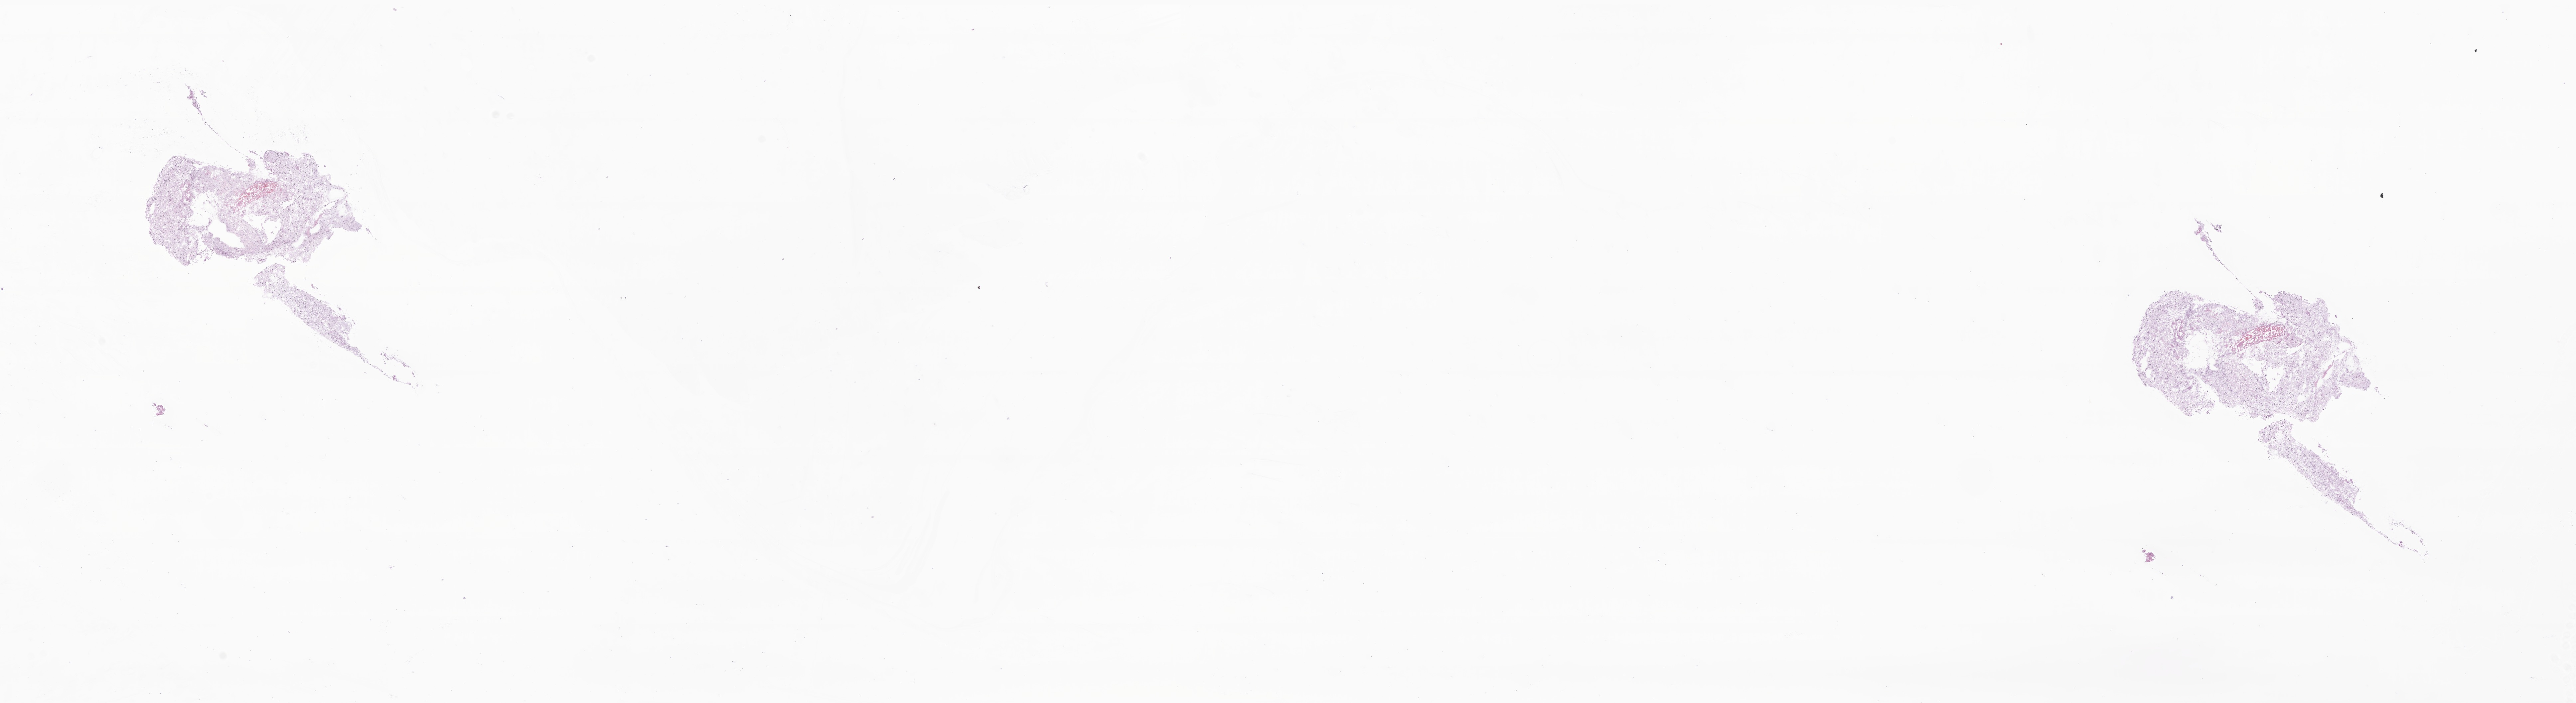
Whole-slide image, haematoxylin and eosin stain of tumor tissue from the cerebellum — shown as a low-resolution overview of the whole scanned area (about 32.7 x 8.9 mm), frozen section. Male patient, age 188 months (15 years 8 months).
- diagnosis: Pilocytic astrocytoma